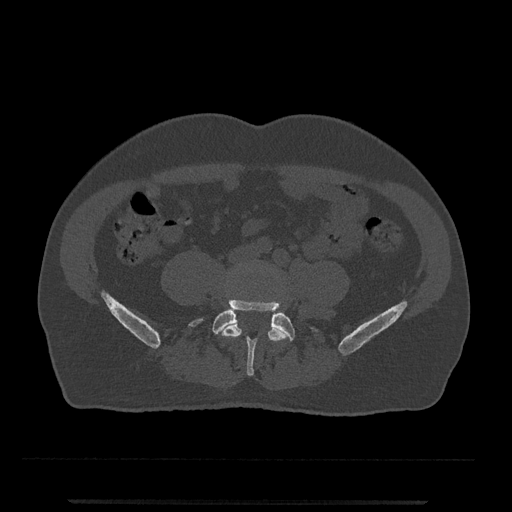
CT including the spine, one axial slice; slice 95 of 797 in the series (ordered by position); 120 kVp; bone window (W 1800 / L 400 HU); 512 × 512 image matrix, field of view 419 × 419 mm. Male patient, age 63 years. From the clinical record (not read from this slice): primary cancer: prostate.
Outlined on this slice (semi-automatic segmentation, software-assisted and operator-edited):
- L4 vertebra: box from (x=221, y=268) to (x=289, y=366) px
- L5 vertebra: (x=190, y=300)–(x=318, y=376)